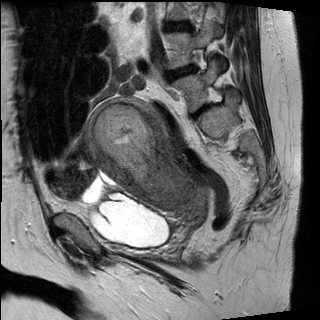
Pelvic MRI for cervical cancer, one sagittal slice. Position 19 of 30 along the scan axis. T2-weighted. 1.5 T. TE 89 ms, TR 2930 ms. 4 mm slice thickness. 320 × 320 image matrix, field of view 260 × 260 mm. Female patient, age 62 years.
Structures marked on this image (manually delineated by an expert):
- uterus and cervix: bounding box (x1, y1, x2, y2) in pixels: (85, 95, 209, 222)